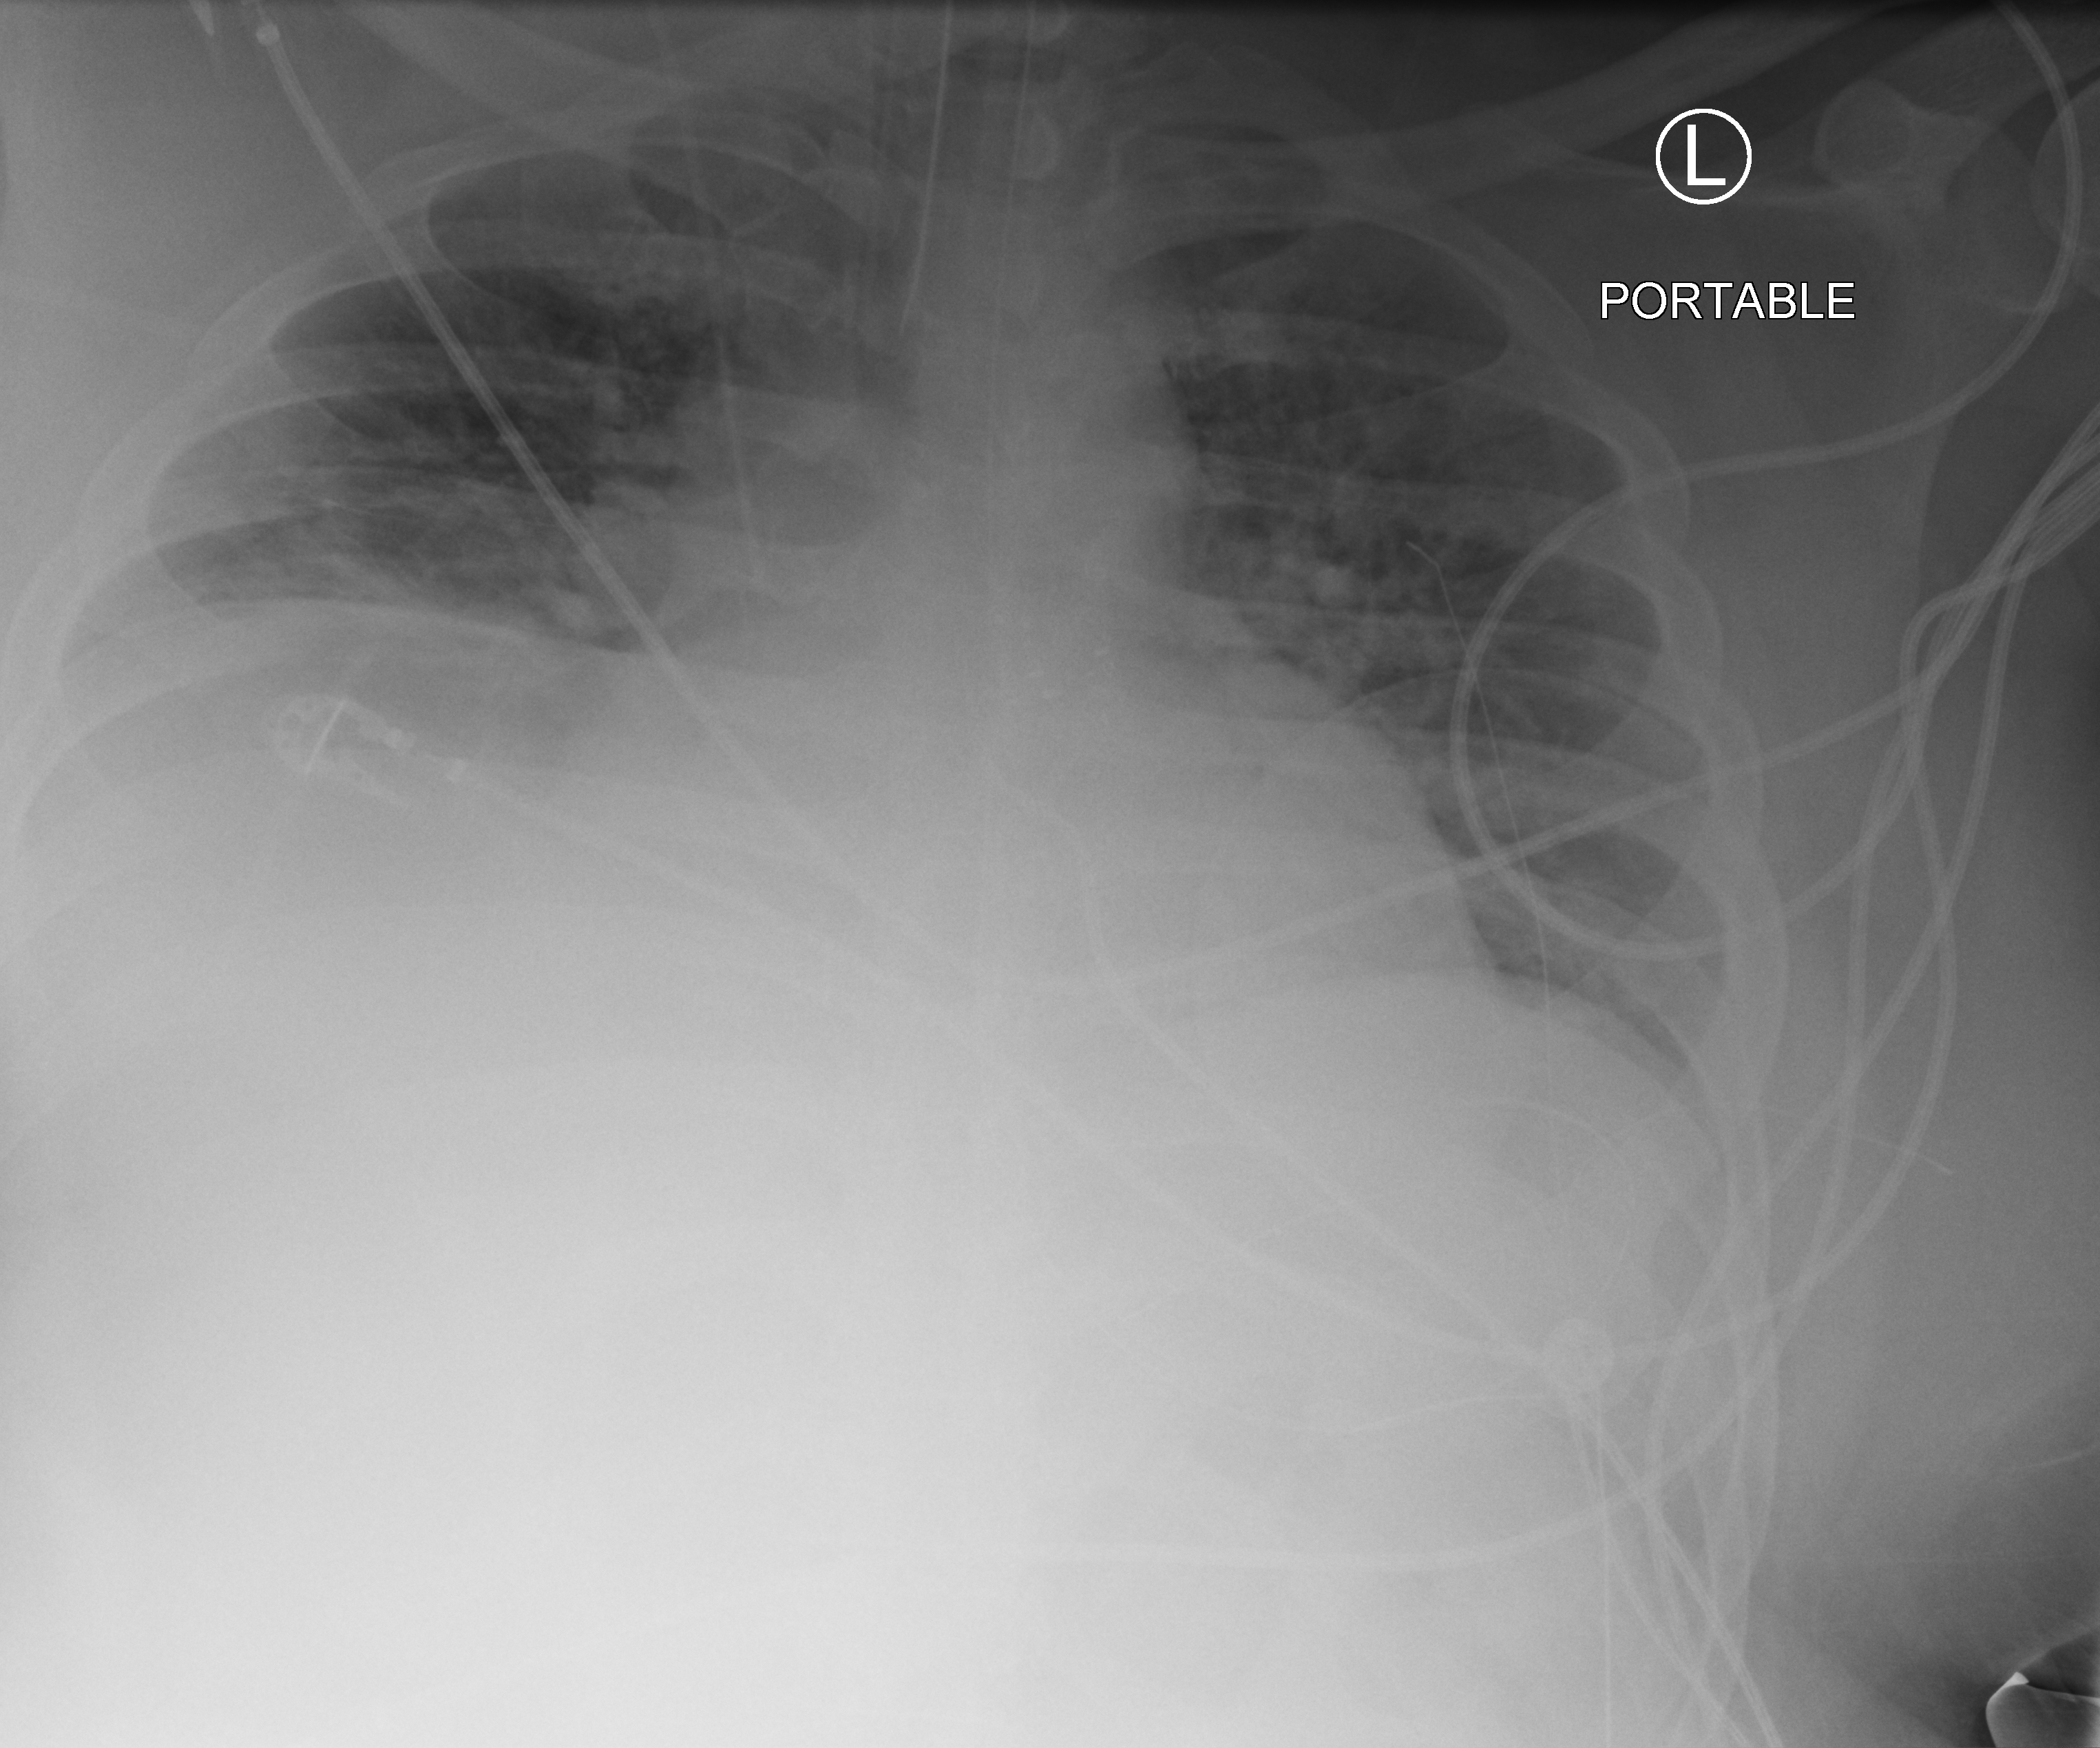
Bedside chest radiograph (computed radiography), anteroposterior (AP) projection. Patient hospitalised with COVID-19; male, aged 18–59 years.
Hospital-stay facts (about this admission, not read from this image; timing relative to this image not recorded): mechanically ventilated during this hospital stay: yes; admitted to intensive care during this hospital stay: yes; COPD (admission record): yes.